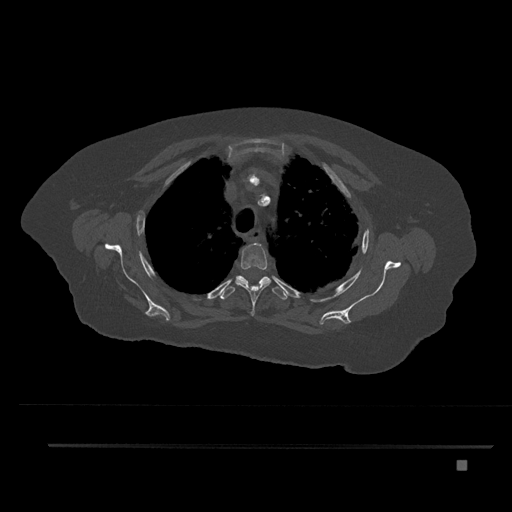
CT including the spine, one axial slice; position 625 of 797 along the scan axis; bone window (W 1800 / L 400 HU); 0.5 mm slice thickness; 512 × 512 image matrix, field of view 437 × 437 mm. Patient: female, 76 years. From the clinical record (not read from this slice): primary cancer: lung; vertebrae with lytic lesions (as recorded): T11, L3.
Outlined on this slice (semi-automatically segmented with operator editing):
- T3 vertebra: bounding box [x1, y1, x2, y2] px = [235, 243, 271, 316]
- T4 vertebra: [220, 275, 287, 300]